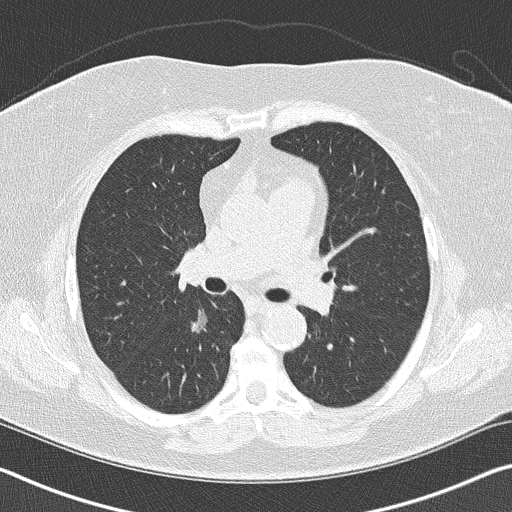
Low-dose screening chest CT, axial slice, baseline annual screen, lung window (W 1500 / L -600 HU), 2 mm slice thickness. Female, age 60 years at enrolment. Former smoker at enrolment.
Lesion marked by an expert reader, bounding box <176,299,226,348> (left, top, right, bottom; pixels). The screening reader recorded 2 non-calcified nodules or masses ≥4 mm on this exam (right lower lobe, left upper lobe); which of them this box marks is not recorded. Official screen result: positive, change unspecified: nodule(s) >= 4 mm or enlarging nodule(s), mass(es), or other non-specific abnormalities suspicious for lung cancer. Later outcome: lung cancer diagnosed 482 days after this screen — bronchiolo-alveolar carcinoma, non-mucinous, right lower lobe, stage IA (AJCC 6th edition), 15 mm at pathology.